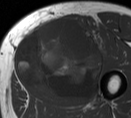
MRI of an extremity soft-tissue mass, one axial slice; position 33 of 55 along the scan axis; MR volume resampled by the dataset authors to the PET/CT grid (not the native acquisition matrix); 131 × 118 image matrix. Male patient. Case-level facts recorded for this patient, not image findings: histological type: pleiomorphic liposarcoma; grade: high; site of the primary tumour: left thigh.
Structures marked on this image (expert contour drawn on MRI and transferred to this co-registered scan by the dataset authors):
- gross tumour volume including surrounding oedema: bounding box [x1, y1, x2, y2] px = [13, 16, 108, 101]
- gross tumour volume (mass): [14, 18, 104, 102]